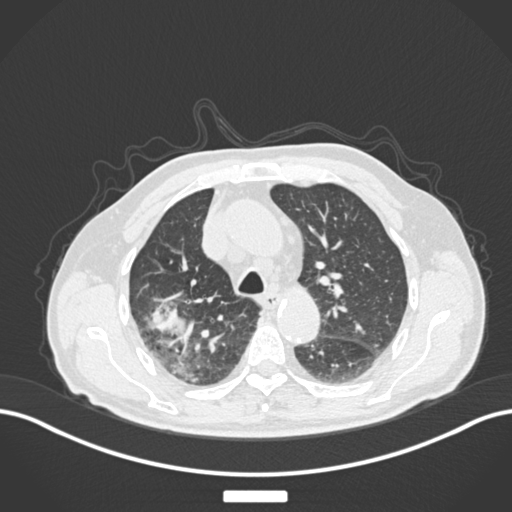
Chest CT, one axial slice. Slice 133 of 201 in the series (ordered by position). Reconstruction kernel B30f. Lung window (W 1500 / L -600 HU). 1 mm slice thickness. 512 × 512 image matrix, field of view 400 × 400 mm. Patient: male, 72 years. From the clinical record (not read from this slice): clinical TNM (as recorded): T3 N2 M0.
Annotated regions visible in this slice (rectangle marked by the reading radiologist):
- lung tumour (recorded histology: adenocarcinoma): bounding box [x1, y1, x2, y2] px = [142, 292, 191, 349]